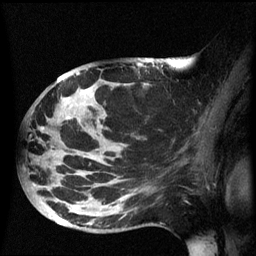
Breast MRI (dynamic contrast-enhanced), one sagittal slice; slice 35 of 60 in the series (ordered by position); dynamic contrast-enhanced series, image 2 of 3 at this slice position (ordered by acquisition); 1.5 T; TE 4.2 ms, TR 8.4 ms; 2.5 mm slice thickness; 256 × 256 image matrix, field of view 220 × 220 mm. Female patient, age 49 years.
Annotated regions visible in this slice (semi-automatically segmented with operator editing):
- analysis volume of interest (the breast-tissue region the enhancement analysis was run in; not a lesion): bounding box <26,72,161,233> (left, top, right, bottom; pixels)
- tumour enhancement mask (voxels above the 70 % enhancement threshold inside the analysis volume of interest): <69,72,80,119>